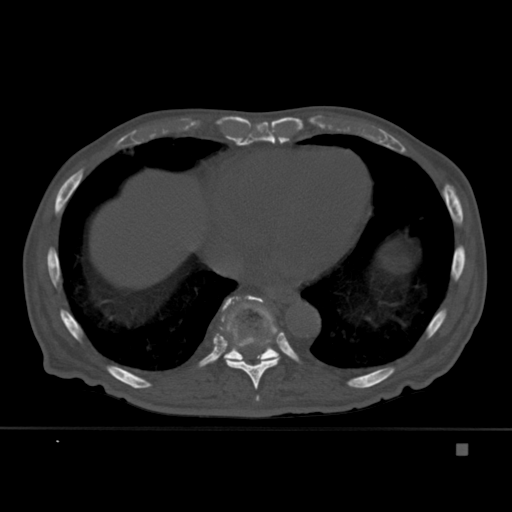
CT including the spine, one axial slice. Slice 242 of 451 in the series (ordered by position). Bone window (W 1800 / L 400 HU). 512 × 512 image matrix, field of view 378 × 378 mm. Patient: male, 75 years. From the clinical record (not read from this slice): primary cancer: prostate.
Annotated regions visible in this slice (semi-automatically segmented with operator editing):
- T10 vertebra: box from (x=222, y=296) to (x=281, y=363) px
- T8 vertebra: (x=256, y=395)–(x=260, y=401)
- T9 vertebra: (x=213, y=295)–(x=287, y=401)